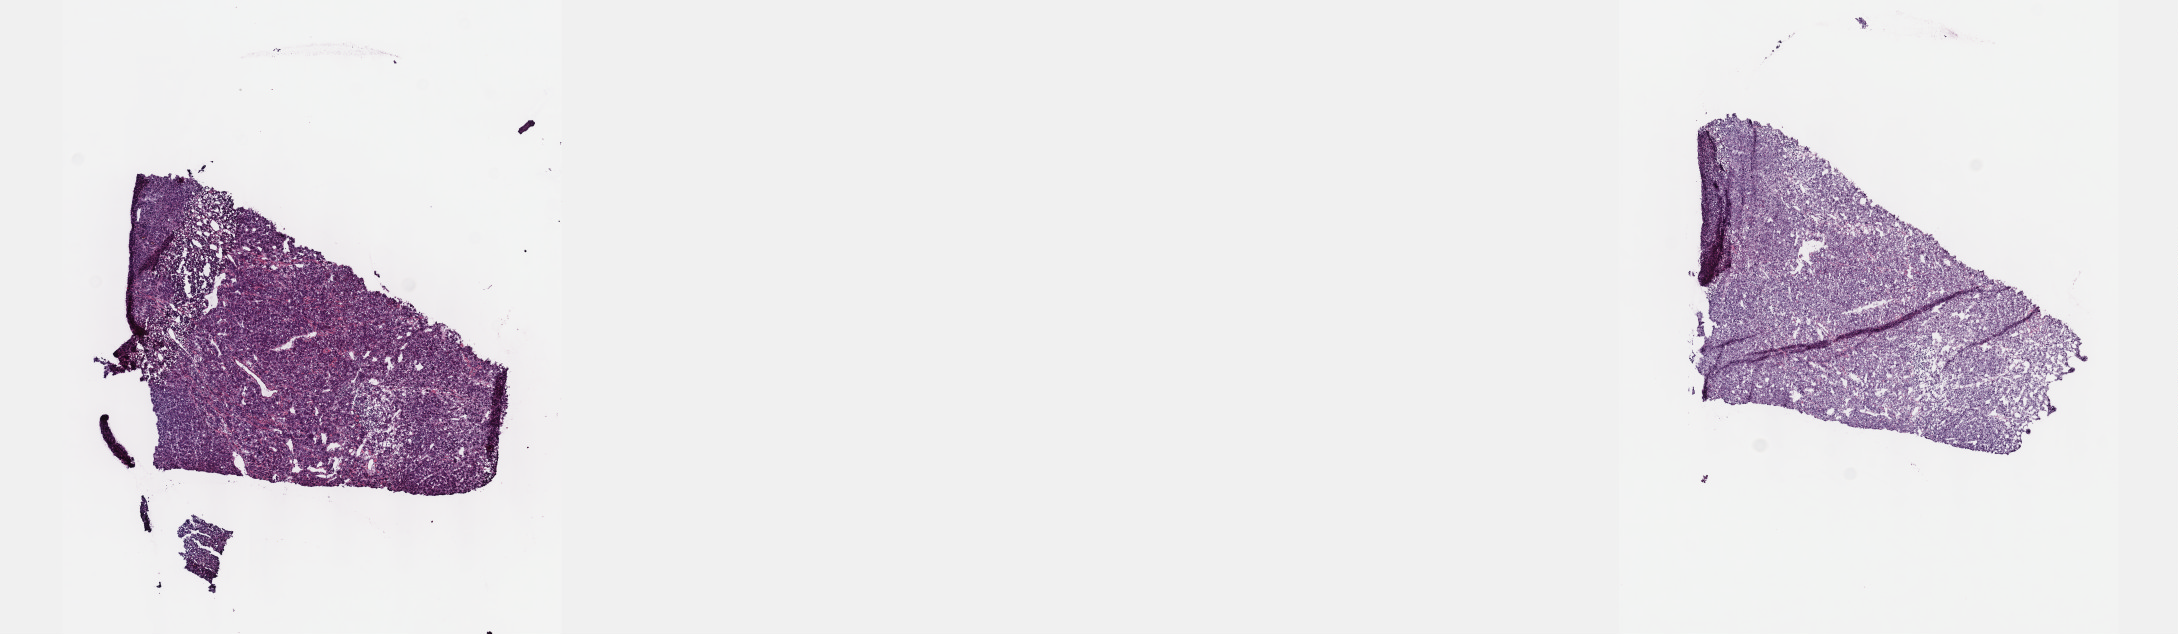
H&E-stained whole-slide image, a low-resolution overview of the entire scanned area, about 17.6 x 5.1 mm. Frozen section from the top of the tissue portion. Sample: primary tumour, liver. Patient: female, age at initial diagnosis 66 years. Histologic grade: G3 (poorly differentiated). Composition of this section per pathologist review: tumour cells 80%, tumour nuclei 80%, normal cells 0%, stromal cells 20%, necrosis 0%. Inflammatory infiltration, as recorded: lymphocyte infiltration 3%, monocyte infiltration 1%, neutrophil infiltration 2%.
TNM: T1 N0 M0. AJCC pathologic stage: I (7th edition). Diagnosis: Hepatocellular carcinoma, NOS.